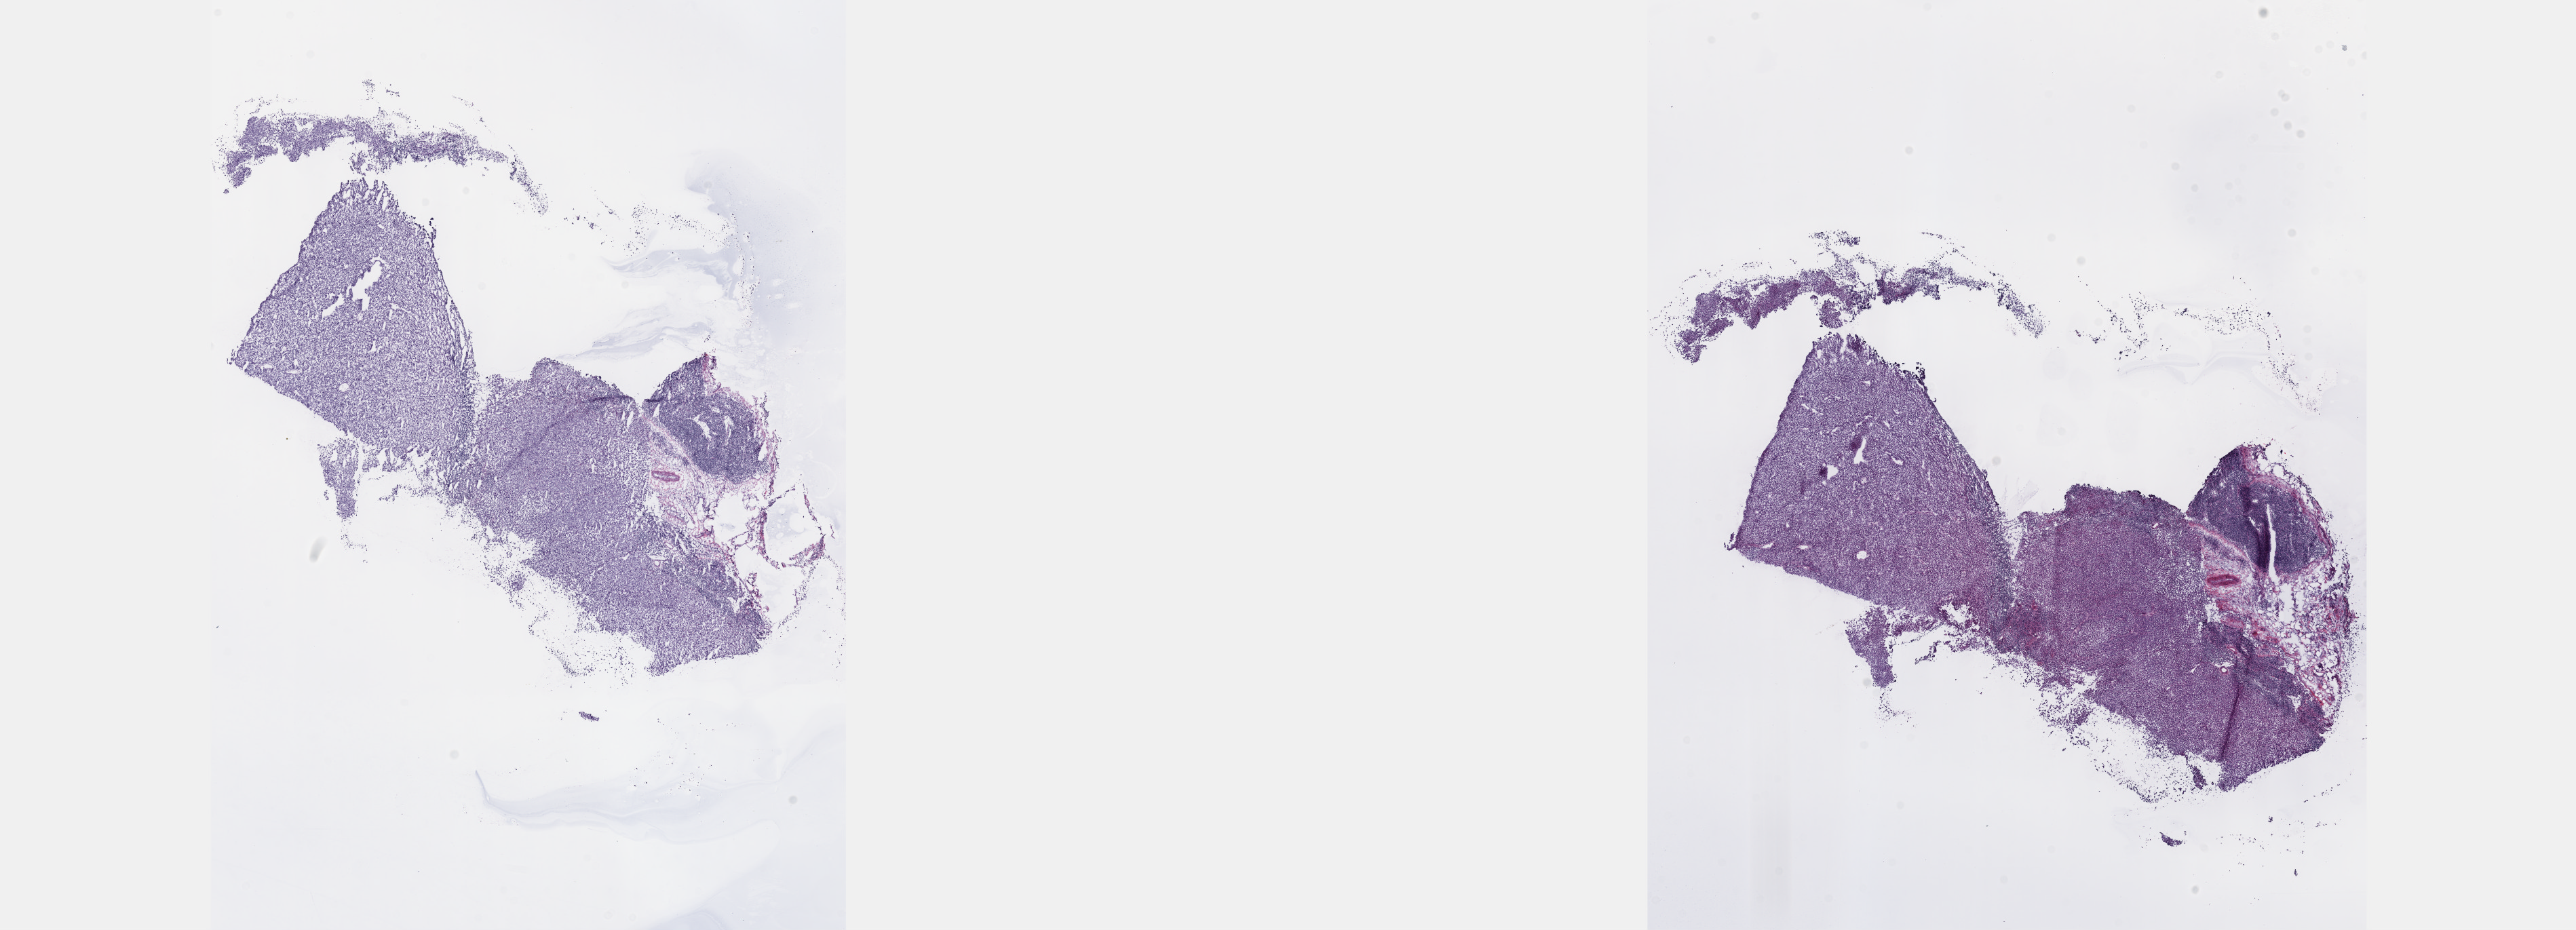
Digitized H&E-stained tissue section (whole slide), a low-resolution overview of the entire scanned area, about 30.7 x 11.1 mm; frozen section from the top of the tissue portion; metastatic tumour sample, sampled site: lymph nodes of axilla or arm. Patient: female, age at initial diagnosis 25 years. Pathologist review of this section (percent, as recorded): tumour cells 70%, tumour nuclei 70%, normal cells 0%, stromal cells 30%, necrosis 0%. Infiltration values recorded for this section: lymphocyte infiltration 9%, monocyte infiltration 2%, neutrophil infiltration 3%.
- this section: metastatic tumour tissue
- patient diagnosis: Malignant melanoma, NOS